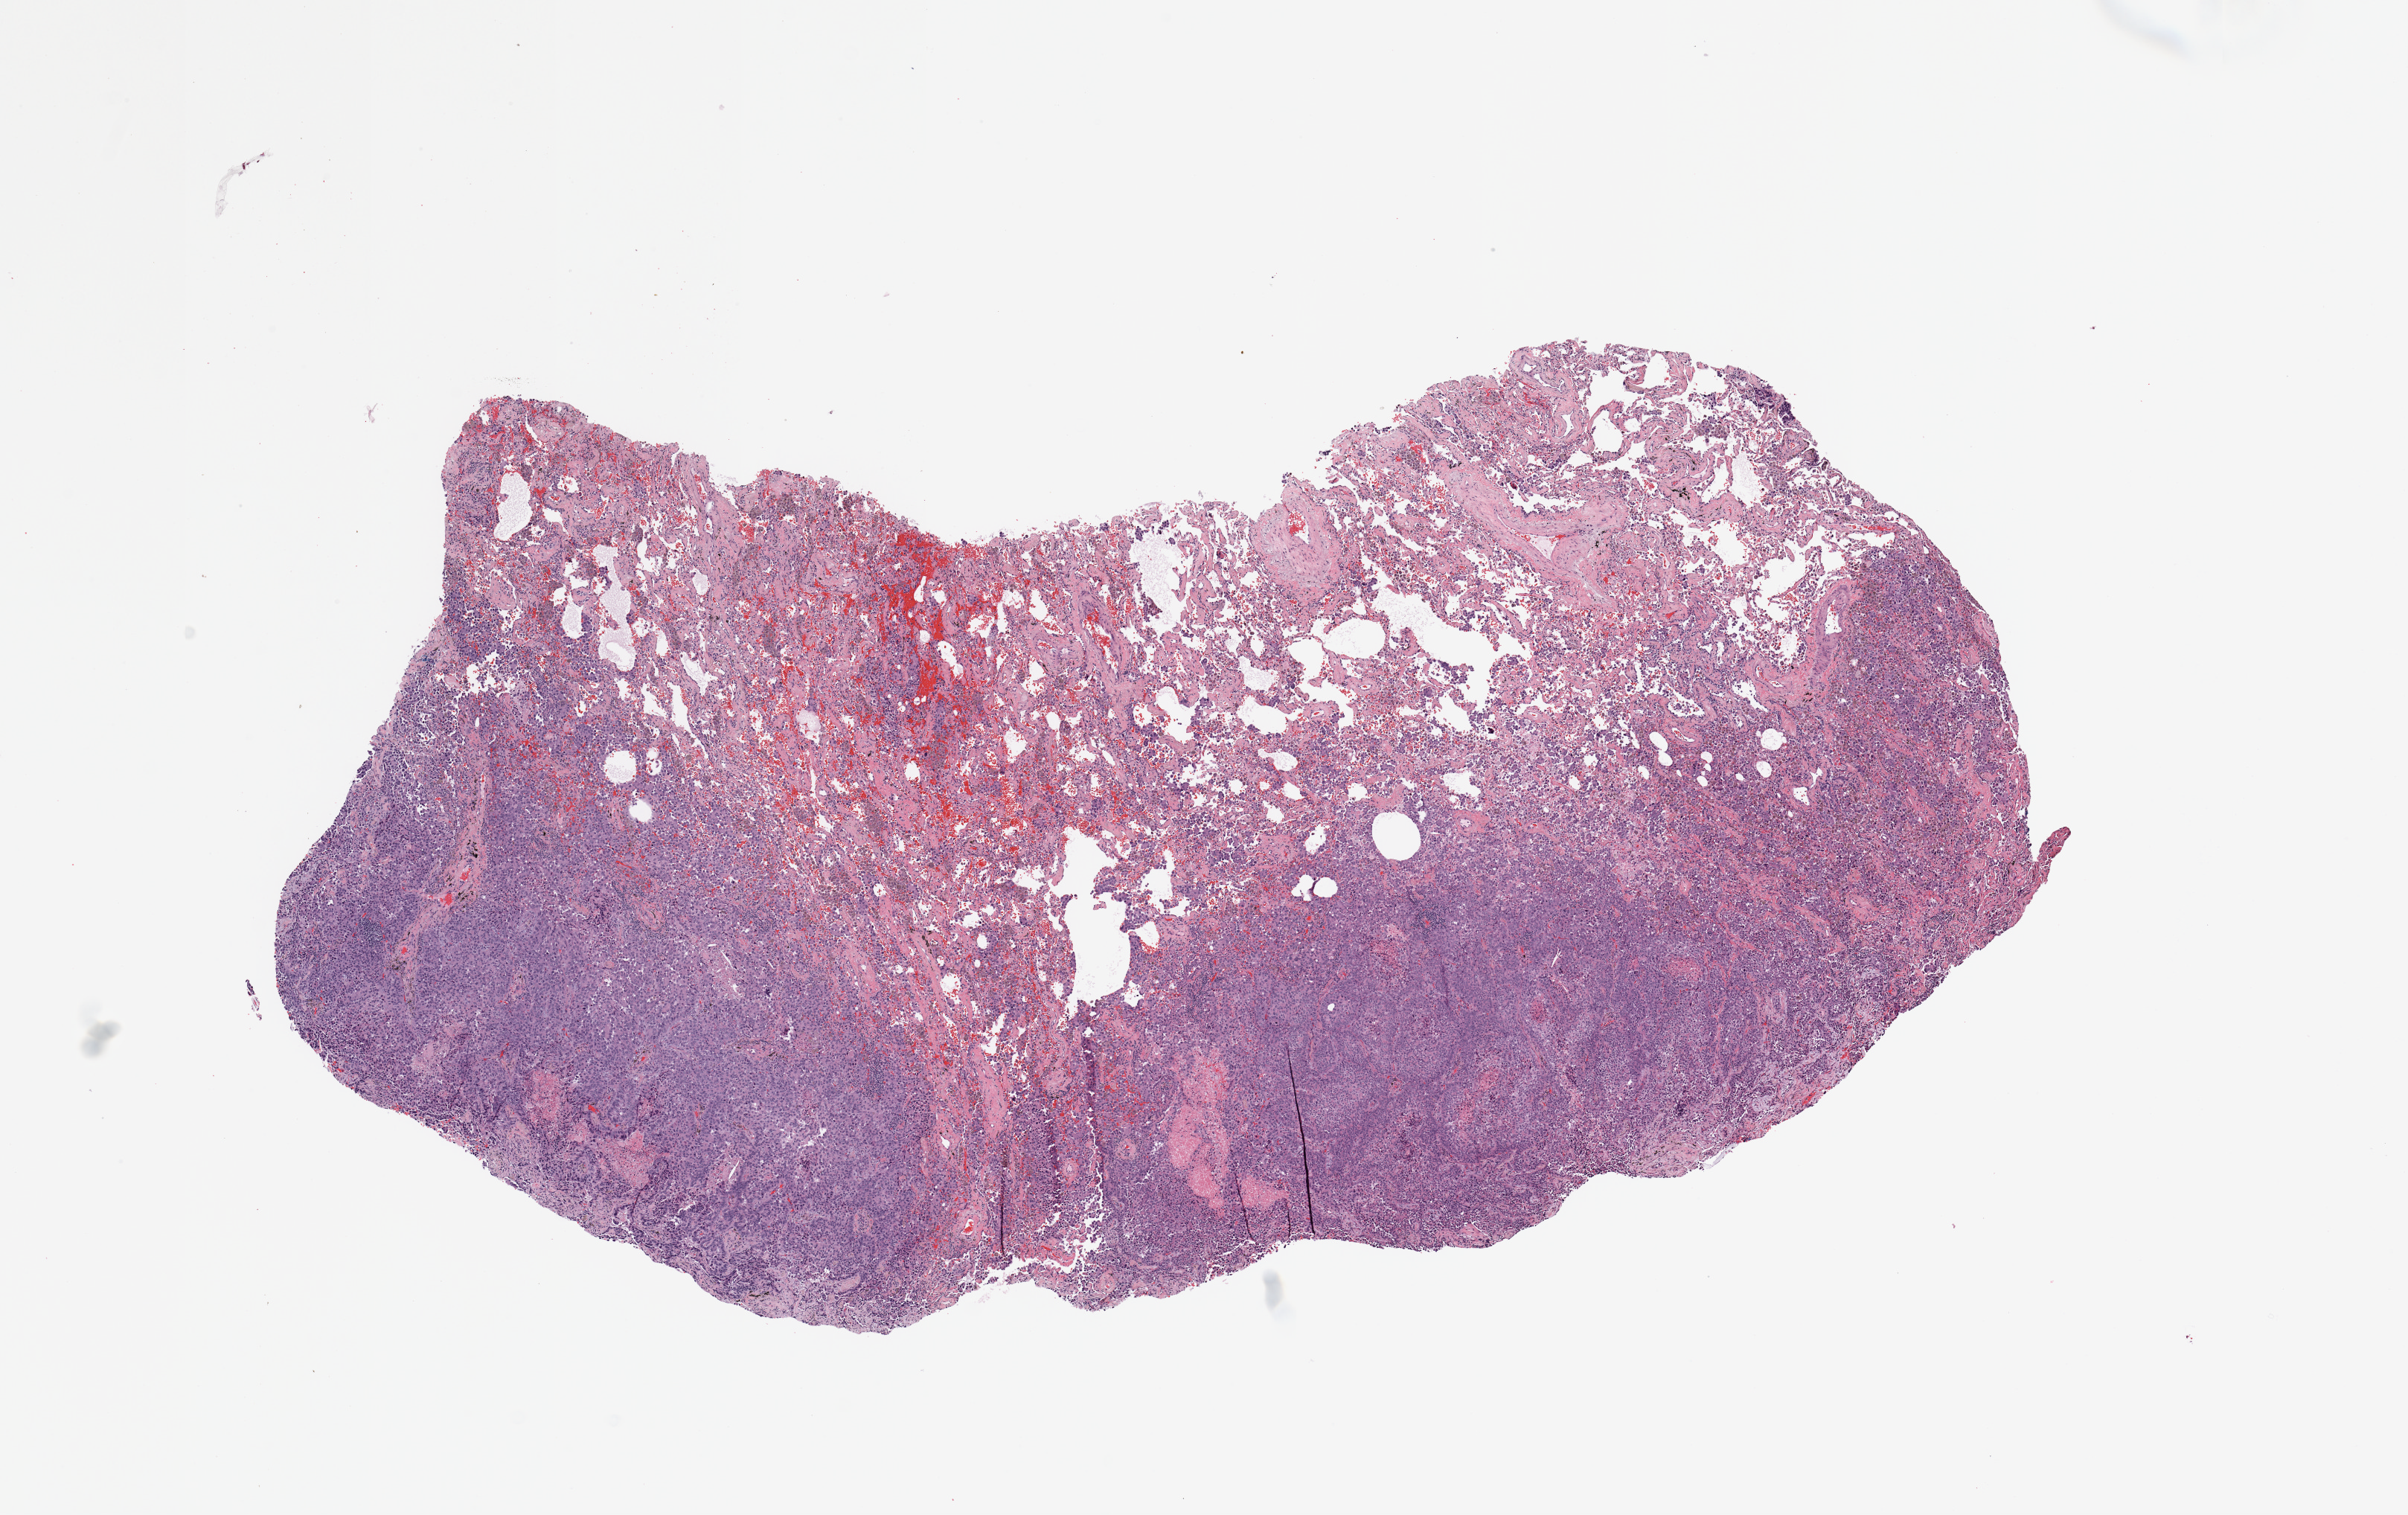
Digitized H&E tissue section (whole slide) — whole scanned area (about 12.8 x 8.1 mm) shown as a low-resolution overview. Tumour tissue sample, lung. 62-year-old female patient. Histologic grade: G3 (poorly differentiated).
Primary tumour site (as recorded): right lower lobe. AJCC pathologic stage: IIB. Diagnosis: Adenocarcinoma, NOS.